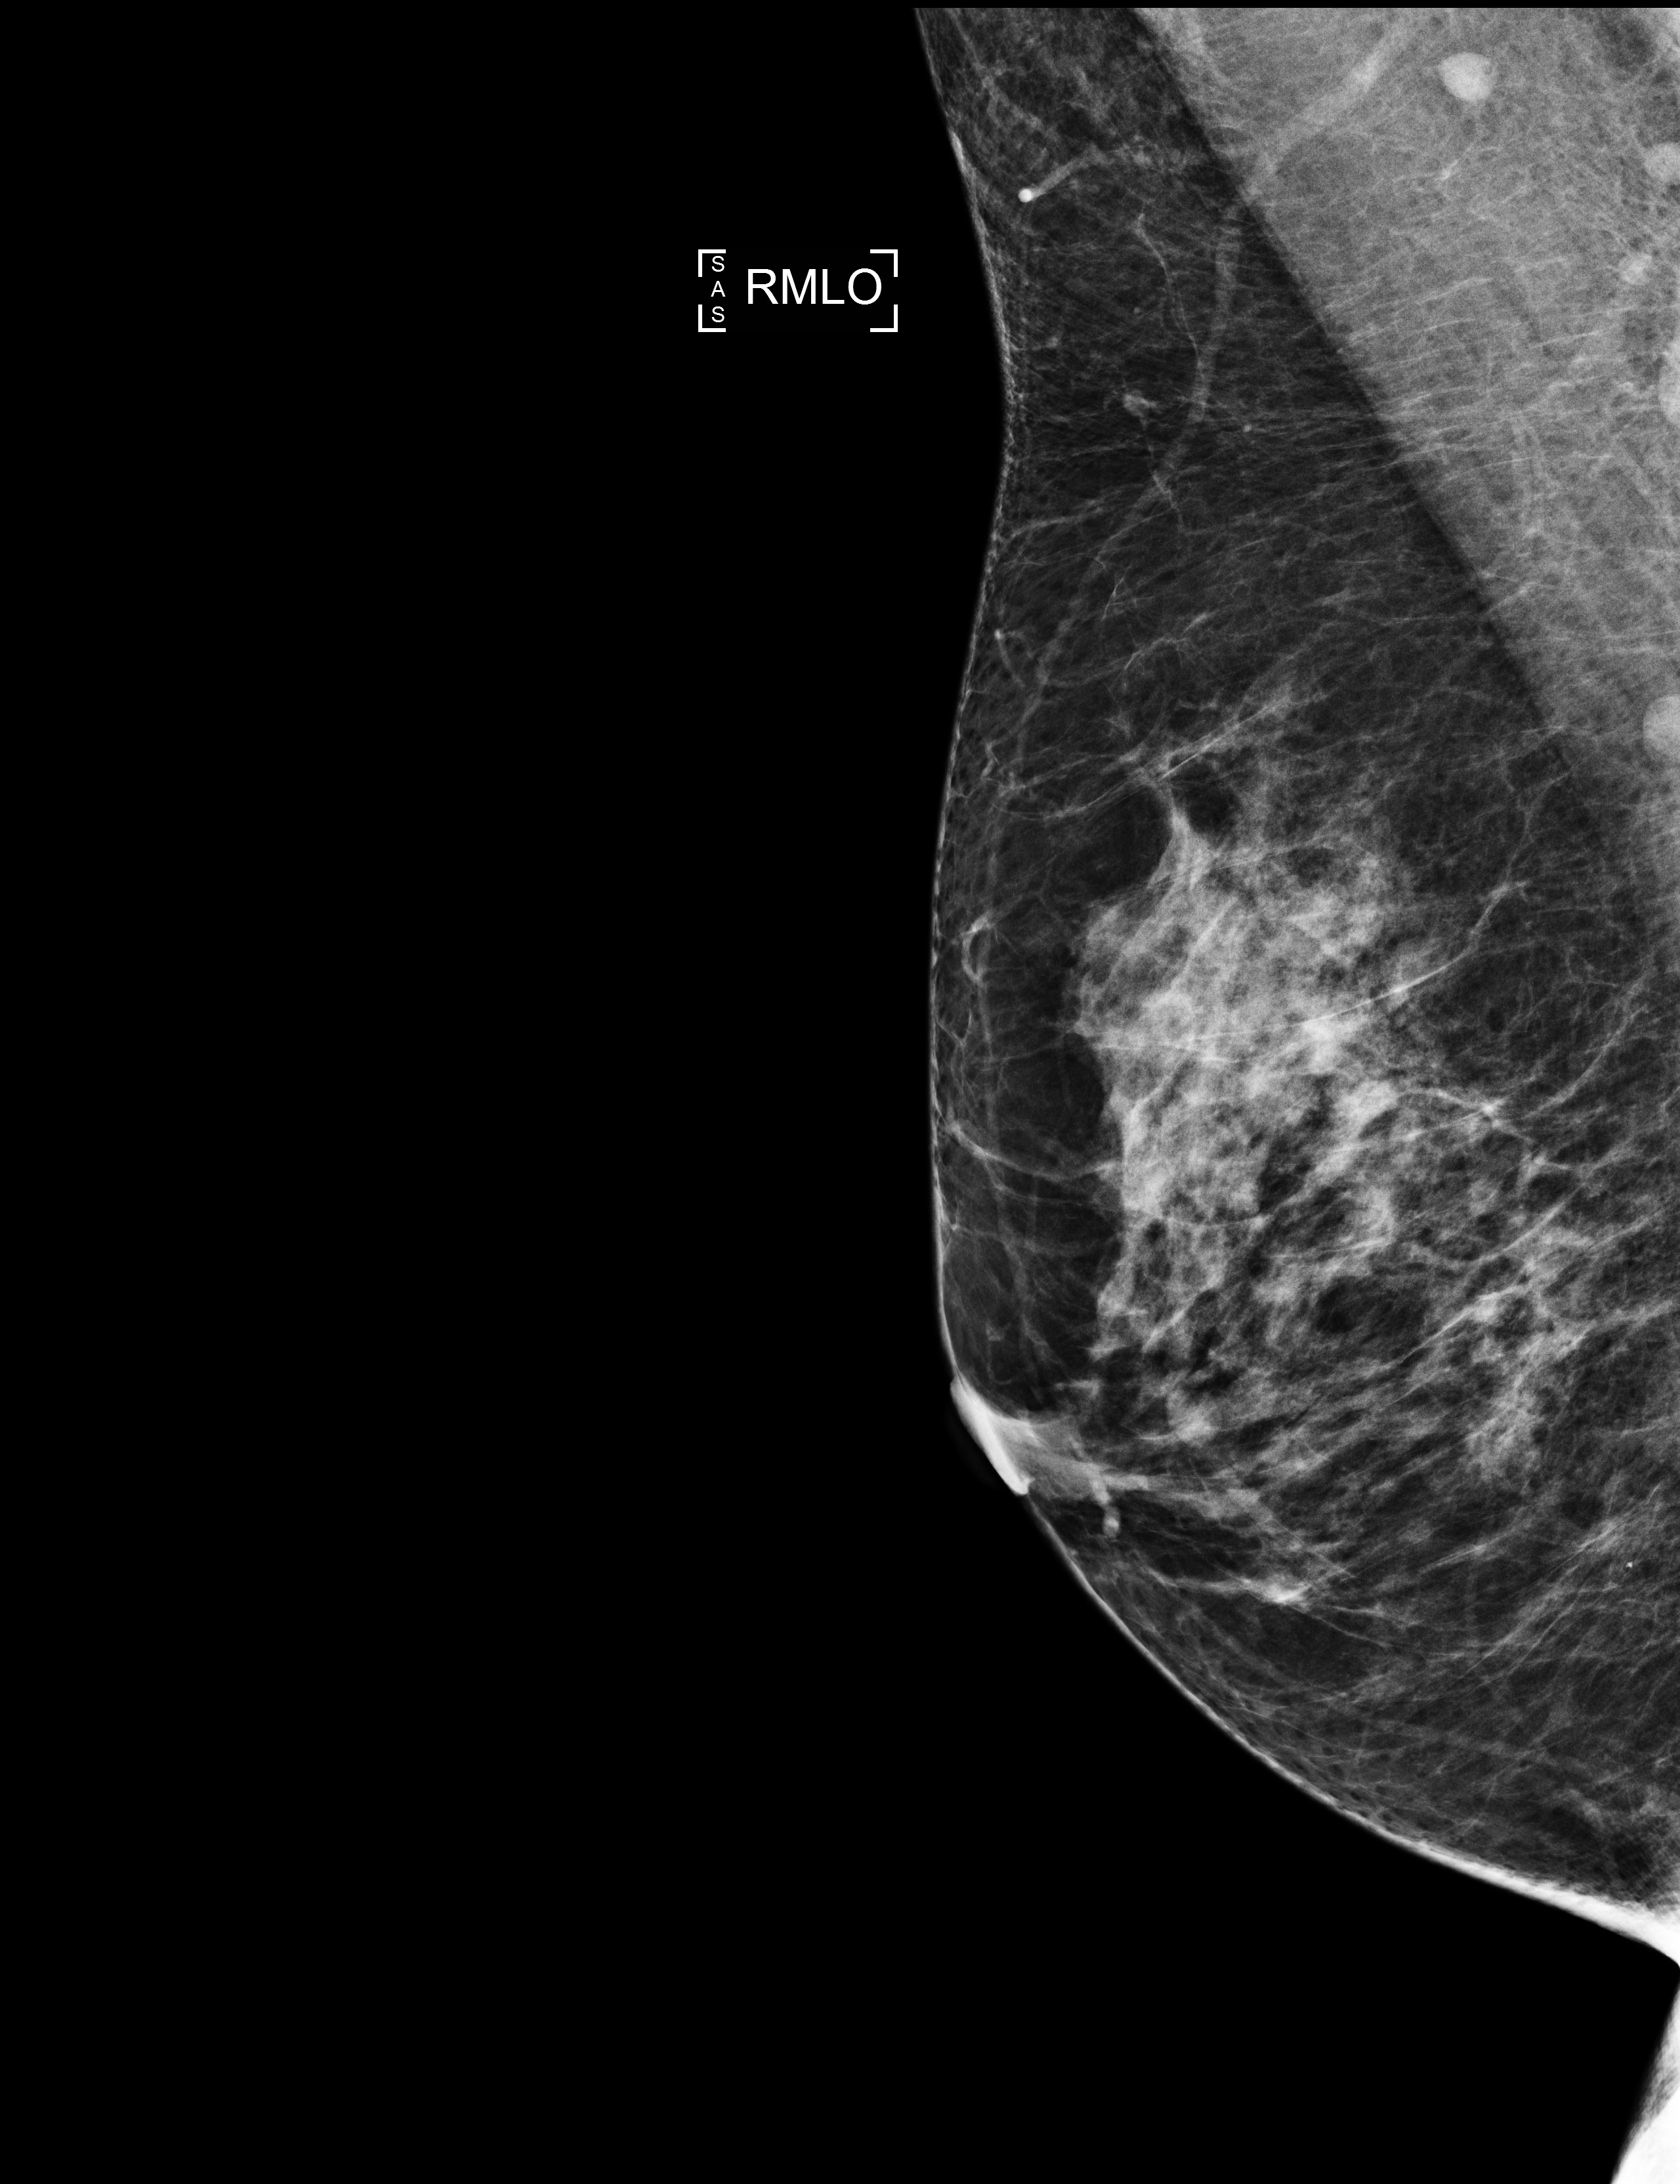
Digital mammogram (FFDM); right breast; medio-lateral oblique projection; annual screening mammography examination; compressed breast thickness 60 mm. Patient aged 54 years (female).
- BI-RADS breast density category at the screening exam (both breasts, scale 1–4): 3
- final BI-RADS assessment for this screening round (tomosynthesis exam, both breasts): category 1
- recall: no recall after this screen